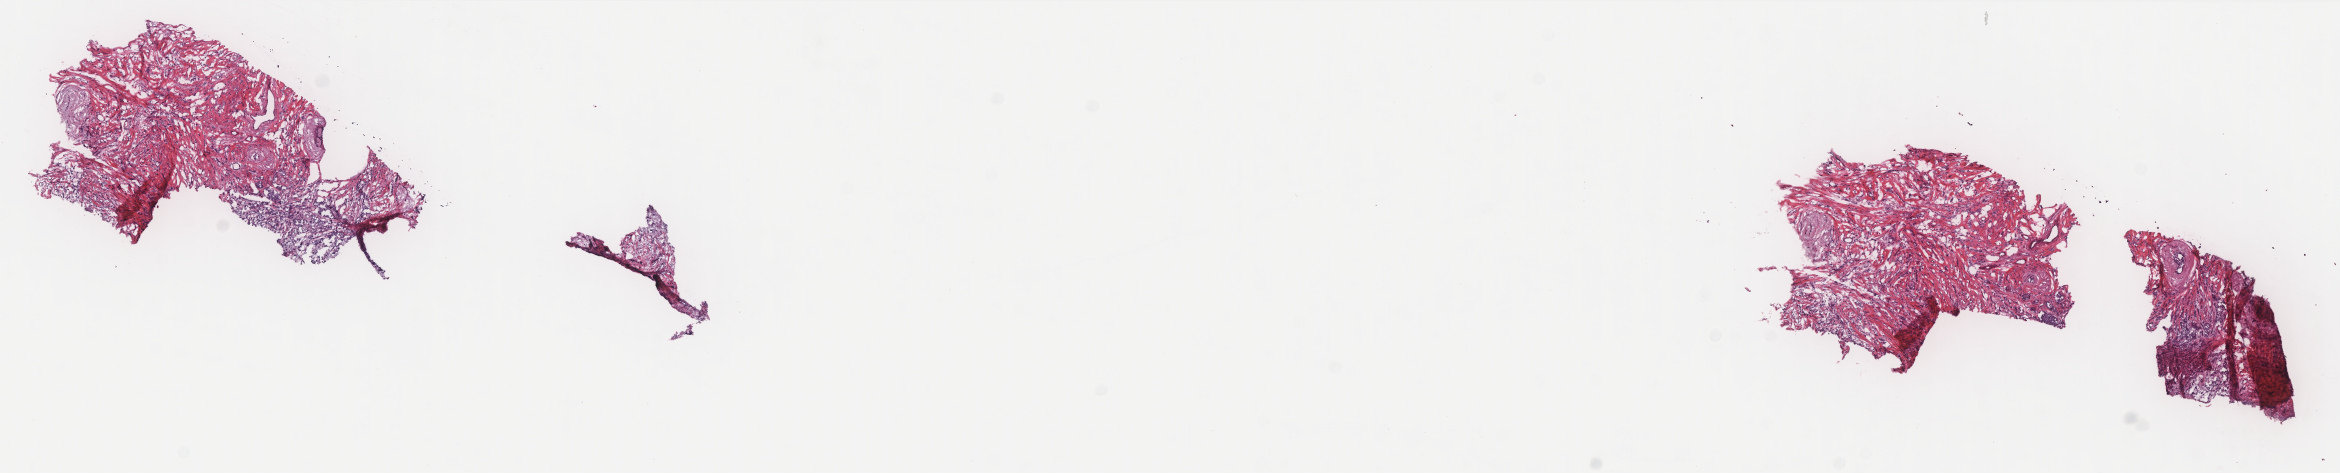
Whole-slide histology image, H&E-stained — shown as a low-resolution overview of the whole scanned area (about 18.8 x 3.8 mm, from a 40x scan); frozen section from the top of the tissue portion; primary tumour sample from the breast. Female patient; age at initial diagnosis 62 years. Composition of this section per pathologist review: tumour cells 80%, tumour nuclei 80%, normal cells 2%, stromal cells 18%, necrosis 0%. Infiltration values recorded for this section: lymphocyte infiltration 2%, monocyte infiltration 0%, neutrophil infiltration 0%.
• histologic diagnosis: Infiltrating duct carcinoma, NOS